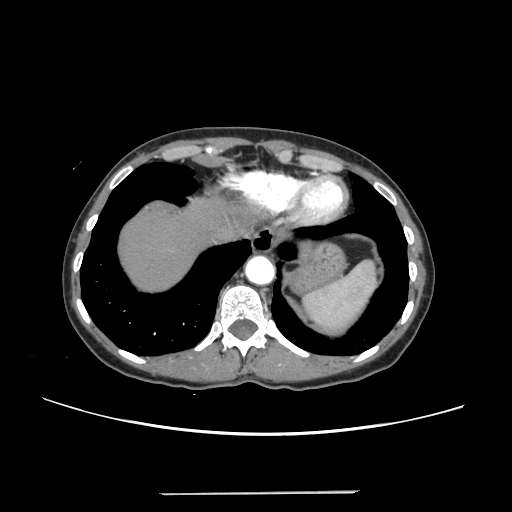
Contrast-enhanced abdominal CT, one axial slice; position 217 of 240 along the scan axis; 120 kVp; intravenous contrast given; soft-tissue window (W 400 / L 40 HU); 1.25 mm slice thickness; 512 × 512 image matrix, field of view 371 × 371 mm. Female patient, age 60 years. Case-level facts recorded for this patient, not image findings: diagnosis: colorectal cancer liver metastases, imaged before liver resection; multiple liver metastases: no; largest metastasis: 1.5 cm; disease in both lobes: no.
Outlined on this slice (manually delineated by an expert):
- liver: bounding box [x1, y1, x2, y2] px = [120, 200, 232, 290]
- planned liver remnant (the part of the liver to remain after resection): [120, 200, 232, 290]